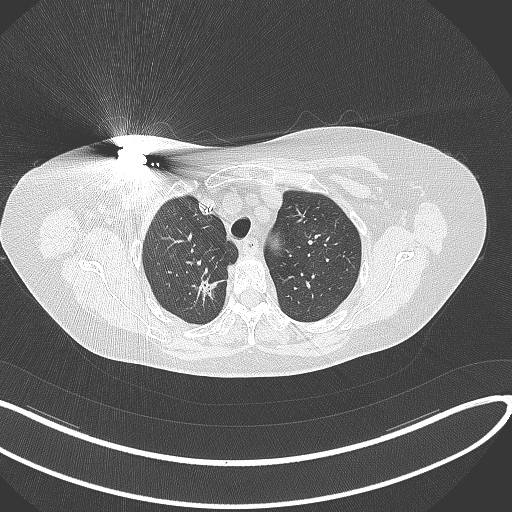
Chest CT, one axial slice. Slice 269 of 316 in the series (ordered by position). 120 kVp. Lung window (W 1500 / L -600 HU). 512 × 512 image matrix, field of view 400 × 400 mm. Female patient, age 72 years. From the clinical record (not read from this slice): clinical TNM (as recorded): T1c N0 M0.
Annotated regions visible in this slice (bounding box drawn by a radiologist):
- lung tumour (recorded histology: adenocarcinoma): bounding box (x1, y1, x2, y2) in pixels: (190, 274, 223, 306)